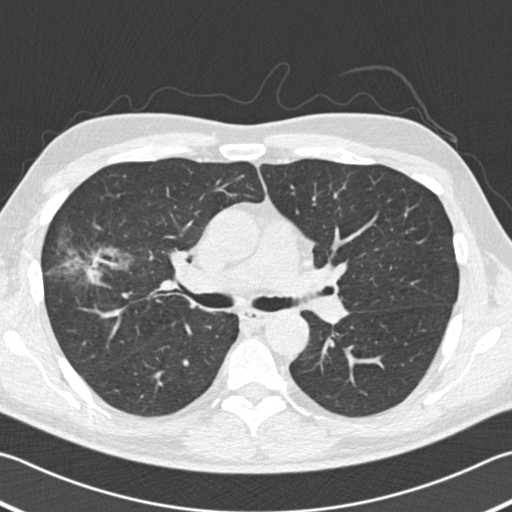
Low-dose screening chest CT, one axial slice. Slice 115 of 182 in the series (ordered by position). Reconstruction kernel B30f. Lung window (W 1500 / L -600 HU). 2 mm slice thickness. 512 × 512 image matrix, field of view 344 × 344 mm.
Outlined on this slice (manually delineated by an expert):
- lesion 1 (tumor, upper lobe of right lung): bounding box [x1, y1, x2, y2] px = [62, 247, 133, 284]